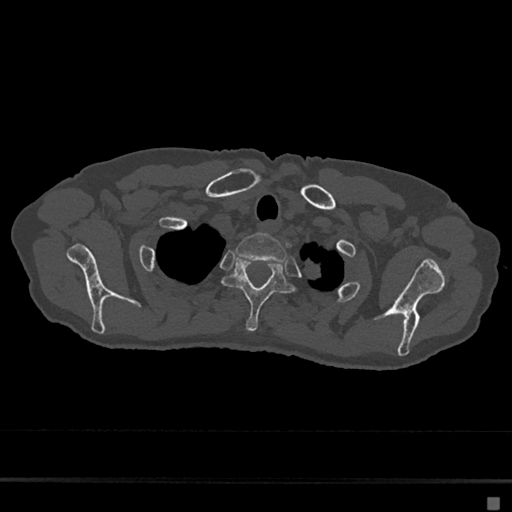
CT including the spine, one axial slice. Slice 581 of 797 in the series (ordered by position). Reconstruction kernel Br40s/3. Bone window (W 1800 / L 400 HU). 0.5 mm slice thickness. 512 × 512 image matrix. Female patient, age 68 years. From the clinical record (not read from this slice): primary cancer: renal.
Annotated regions visible in this slice (semi-automatically segmented with operator editing):
- T1 vertebra: box from (x=236, y=233) to (x=287, y=263) px
- T2 vertebra: (x=222, y=255)–(x=294, y=332)